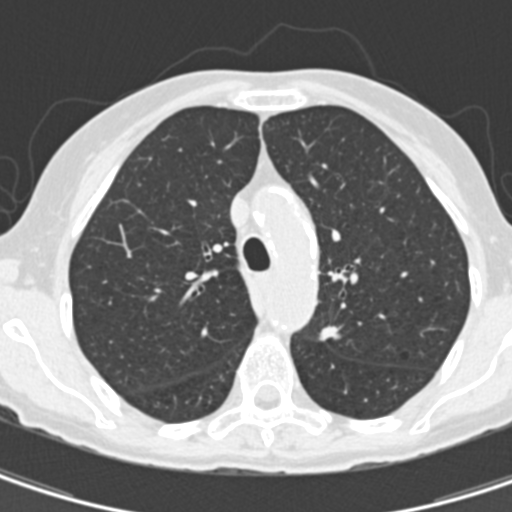
Low-dose screening chest CT, one axial slice; position 109 of 157 along the scan axis; reconstruction kernel B30f; lung window (W 1500 / L -600 HU); 512 × 512 image matrix, field of view 260 × 260 mm.
Structures marked on this image (outlined manually by an expert reader):
- lesion 1 (tumor, upper lobe of left lung): bounding box (x1, y1, x2, y2) in pixels: (319, 326, 341, 341)